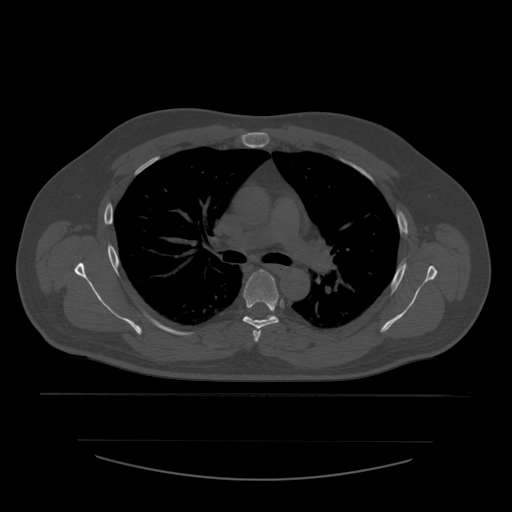
CT including the spine, one axial slice. Position 399 of 532 along the scan axis. Reconstruction kernel STANDARD. 120 kVp. Bone window (W 1800 / L 400 HU). 1.25 mm slice thickness. 512 × 512 image matrix, field of view 441 × 441 mm. Patient age 44 years. Case-level facts recorded for this patient, not image findings: primary cancer: soft tissue sarcoma.
Structures marked on this image (semi-automatically segmented with operator editing):
- T4 vertebra: bounding box <253,327,262,342> (left, top, right, bottom; pixels)
- T5 vertebra: <243,270,279,329>